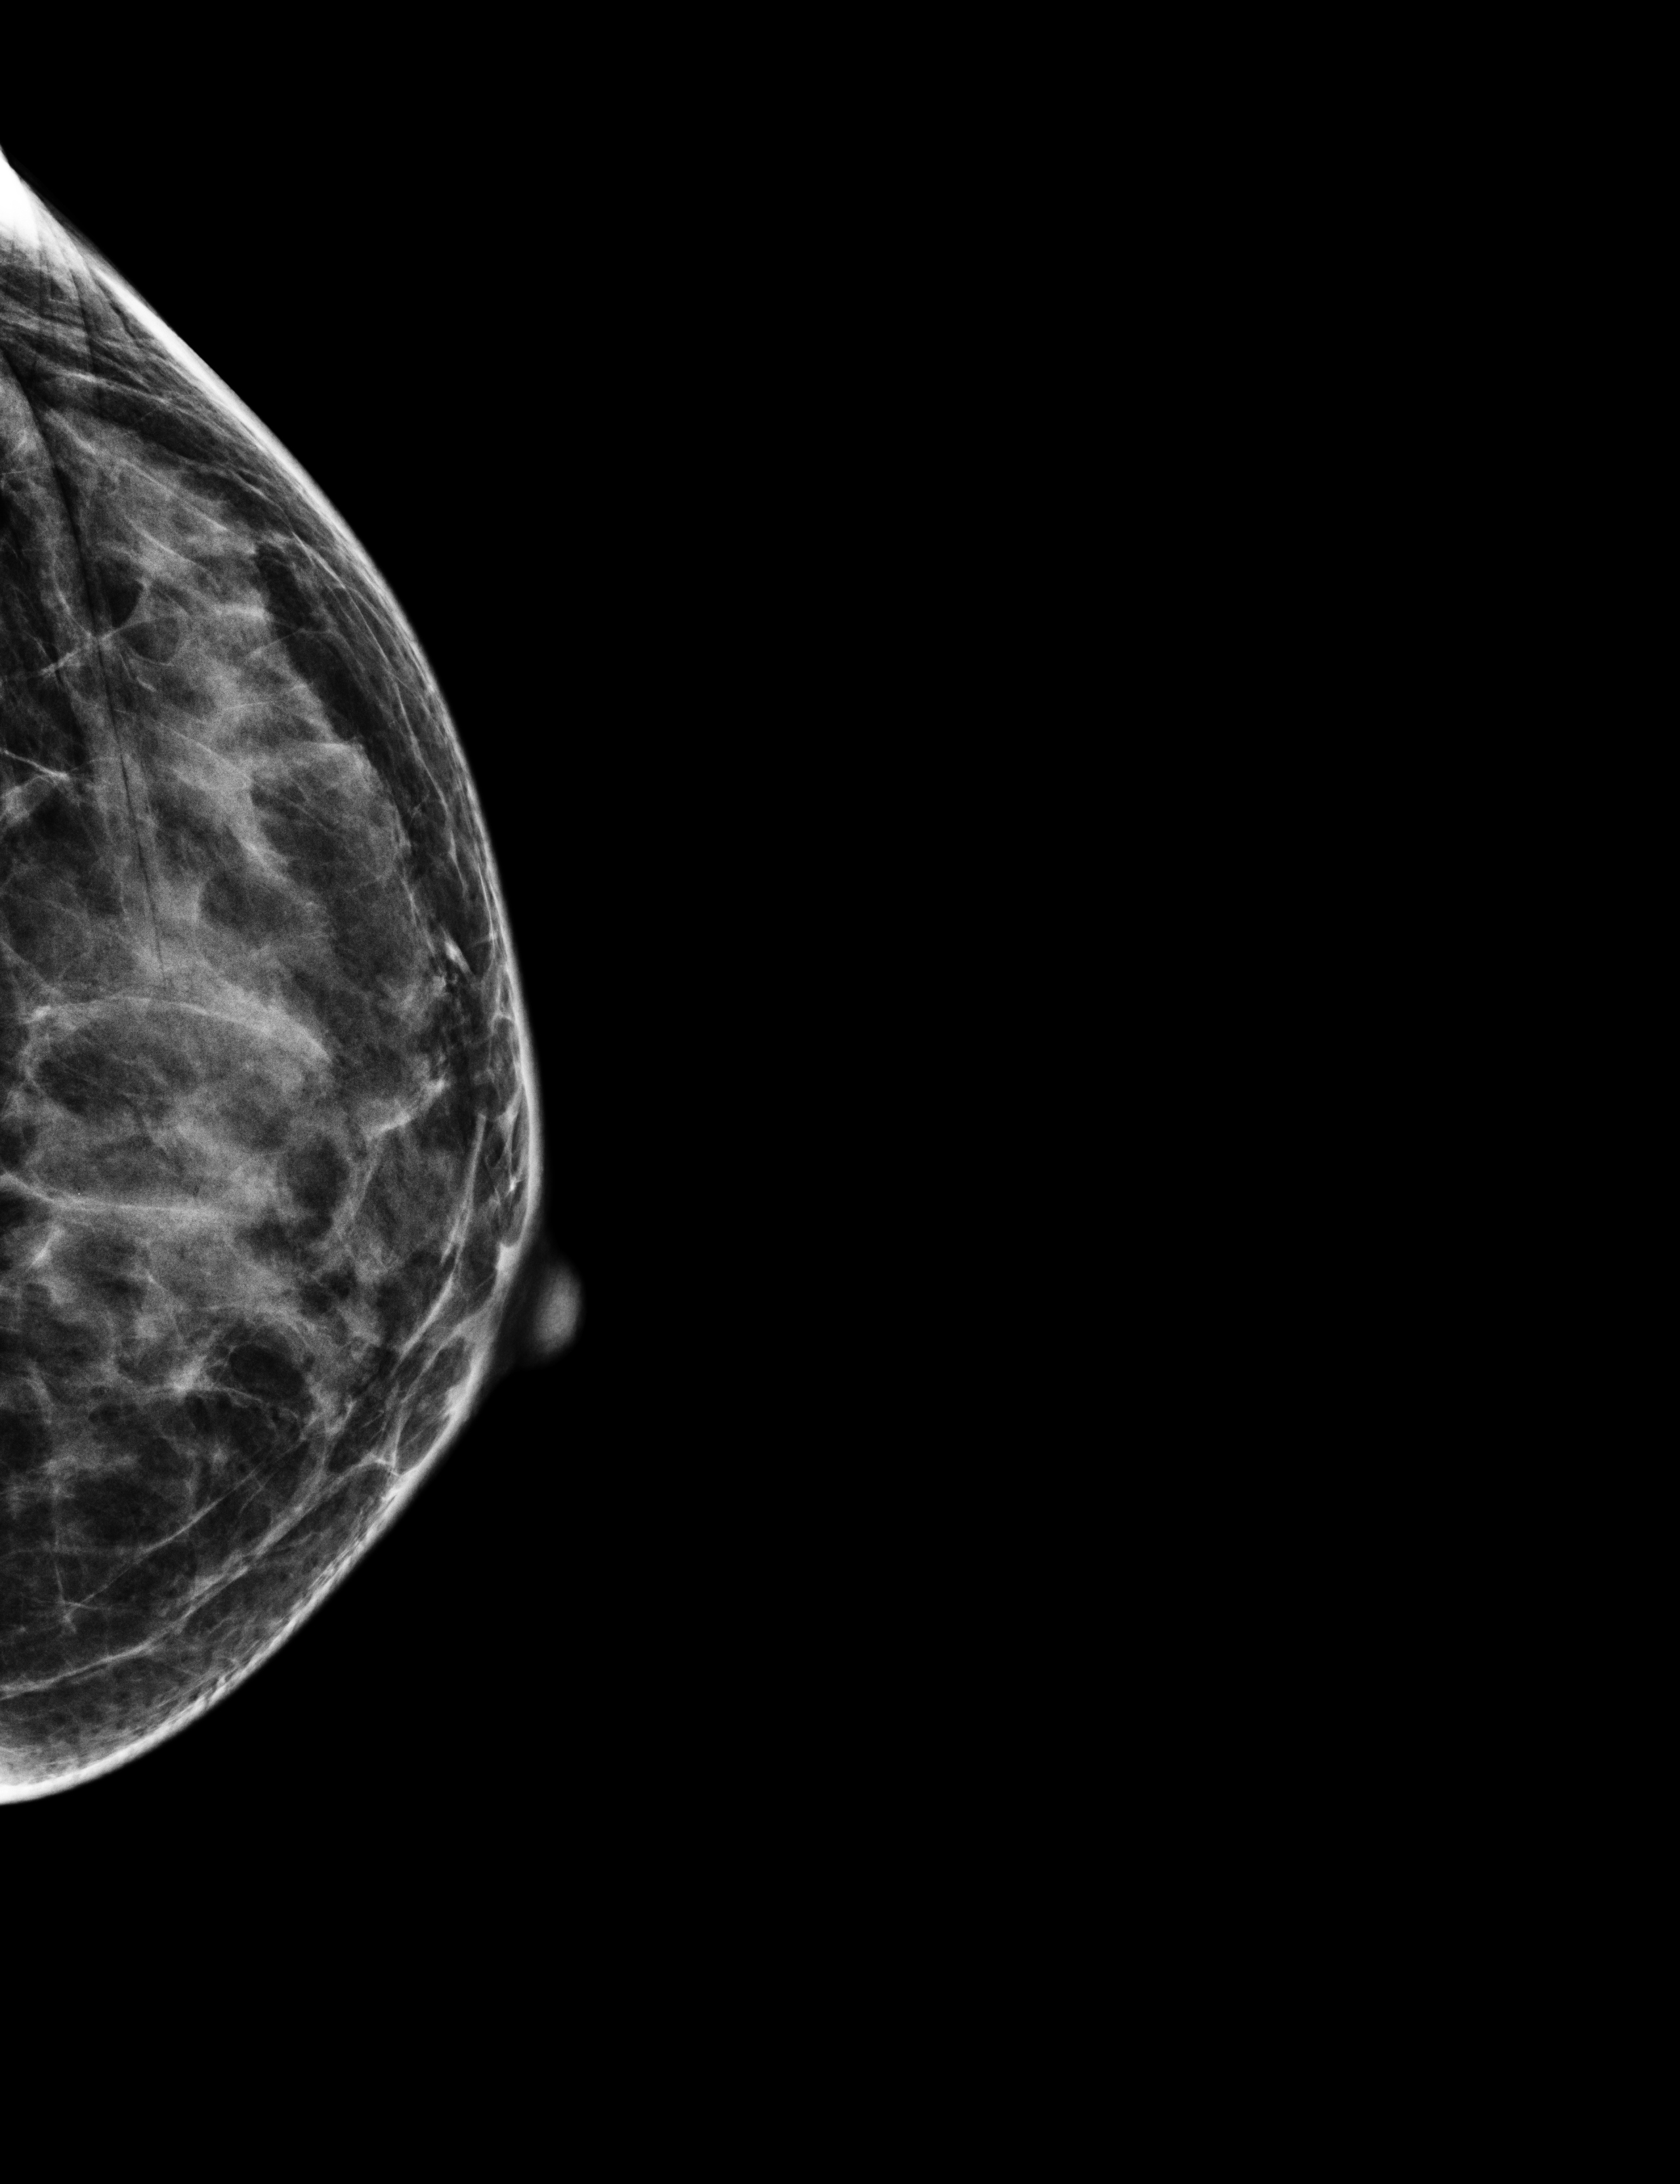
Digital mammogram (FFDM), left breast, exaggerated CC view (lateral), screening examination, compressed breast thickness 32 mm. Female patient, age 52 years.
- BI-RADS breast density category at the screening exam (both breasts, scale 1–4): 3
- final BI-RADS assessment for this screening round (tomosynthesis exam, both breasts): category 1
- recall: no recall after this screen